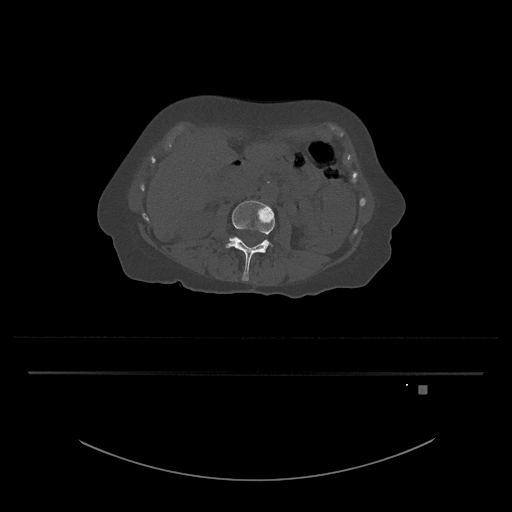
CT including the spine, one axial slice. Slice 424 of 797 in the series (ordered by position). Reconstruction kernel Br40s/3. 120 kVp. Bone window (W 1800 / L 400 HU). 512 × 512 image matrix, field of view 500 × 500 mm. Patient: female, 57 years. Case-level facts recorded for this patient, not image findings: primary cancer: cervical.
Outlined on this slice (semi-automatically segmented with operator editing):
- L3 vertebra: bounding box [x1, y1, x2, y2] px = [225, 200, 275, 281]